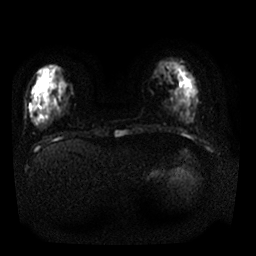
Breast MRI, one axial slice. Slice 6 of 25 in the series (ordered by position). Diffusion-weighted series; image 2 of 4 stored at this slice position (different b-values; order by instance number). 1.5 T. 4 mm slice thickness. 256 × 256 image matrix. Female patient.
Annotated regions visible in this slice (manually delineated by an expert):
- tumour on diffusion-weighted imaging: bounding box [x1, y1, x2, y2] px = [182, 95, 189, 101]